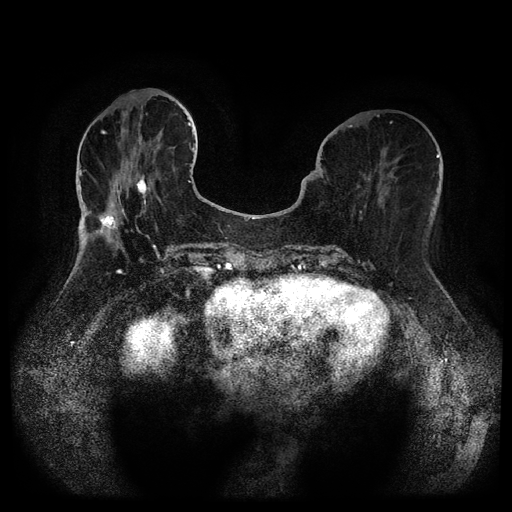
Breast MRI (dynamic contrast-enhanced, multi-phase), one axial slice; position 37 of 116 along the scan axis; dynamic contrast-enhanced series, time point 2 of 5 at this slice position (early post-contrast); 1.5 T; TE 2.6 ms, TR 5.3 ms; 2 mm slice thickness; 512 × 512 image matrix, field of view 350 × 350 mm. Patient: female, 75 years.
Structures marked on this image (semi-automatically segmented with operator editing):
- breast lesion (labelled benign in the annotation): bounding box (x1, y1, x2, y2) in pixels: (131, 175, 150, 198)
- breast lesion (labelled benign in the annotation): (96, 212, 118, 234)